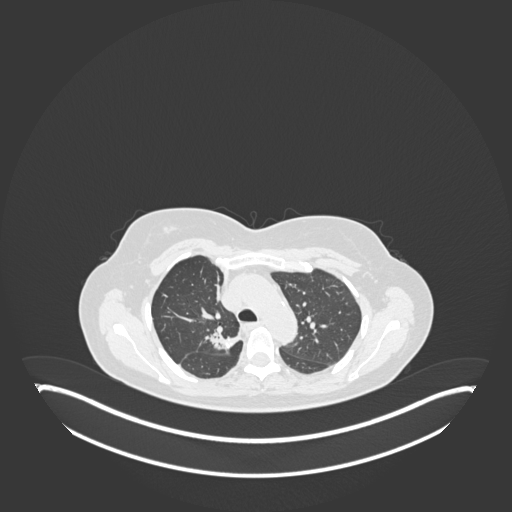
Chest CT, one axial slice. Position 126 of 181 along the scan axis. 120 kVp. Lung window (W 1500 / L -600 HU). 1 mm slice thickness. 512 × 512 image matrix, field of view 500 × 500 mm. Patient: female, 65 years. From the clinical record (not read from this slice): clinical TNM (as recorded): T1b N0 M0.
Outlined on this slice (rectangle marked by the reading radiologist):
- lung tumour (recorded histology: adenocarcinoma): box from (x=205, y=319) to (x=241, y=359) px